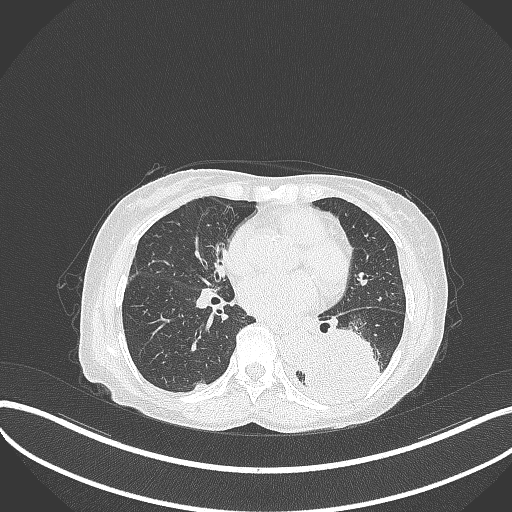
Chest CT, one axial slice; slice 140 of 370 in the series (ordered by position); lung window (W 1500 / L -600 HU); 1 mm slice thickness; 512 × 512 image matrix, field of view 400 × 400 mm. Female patient, age 78 years. From the clinical record (not read from this slice): clinical TNM (as recorded): T3 N0 M1.
Outlined on this slice (bounding box drawn by a radiologist):
- lung tumour (recorded histology: squamous cell carcinoma): box from (x=304, y=323) to (x=387, y=407) px